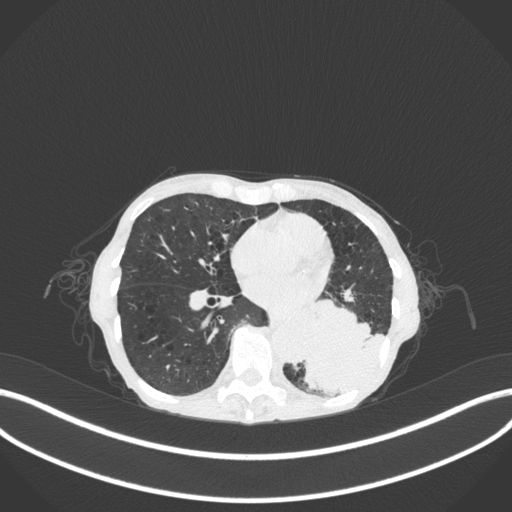
Chest CT, one axial slice. Position 114 of 347 along the scan axis. 120 kVp. Lung window (W 1500 / L -600 HU). 512 × 512 image matrix. Female patient, age 70 years. Case-level facts recorded for this patient, not image findings: clinical TNM (as recorded): T3 N0 M0; histopathological grade: G3.
Outlined on this slice (rectangle marked by the reading radiologist):
- lung tumour (recorded histology: small cell carcinoma): bounding box <302,292,387,395> (left, top, right, bottom; pixels)